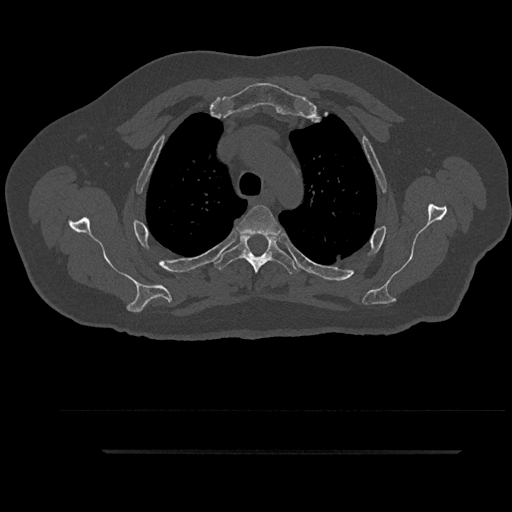
CT including the spine, one axial slice. Position 690 of 797 along the scan axis. Reconstruction kernel Br40s/3. Bone window (W 1800 / L 400 HU). 512 × 512 image matrix, field of view 432 × 432 mm. Male patient, age 63 years. Case-level facts recorded for this patient, not image findings: primary cancer: renal; vertebrae with lytic lesions (as recorded): T8.
Outlined on this slice (semi-automatically segmented with operator editing):
- T3 vertebra: bounding box <236,205,281,238> (left, top, right, bottom; pixels)
- T4 vertebra: <213,235,300,274>